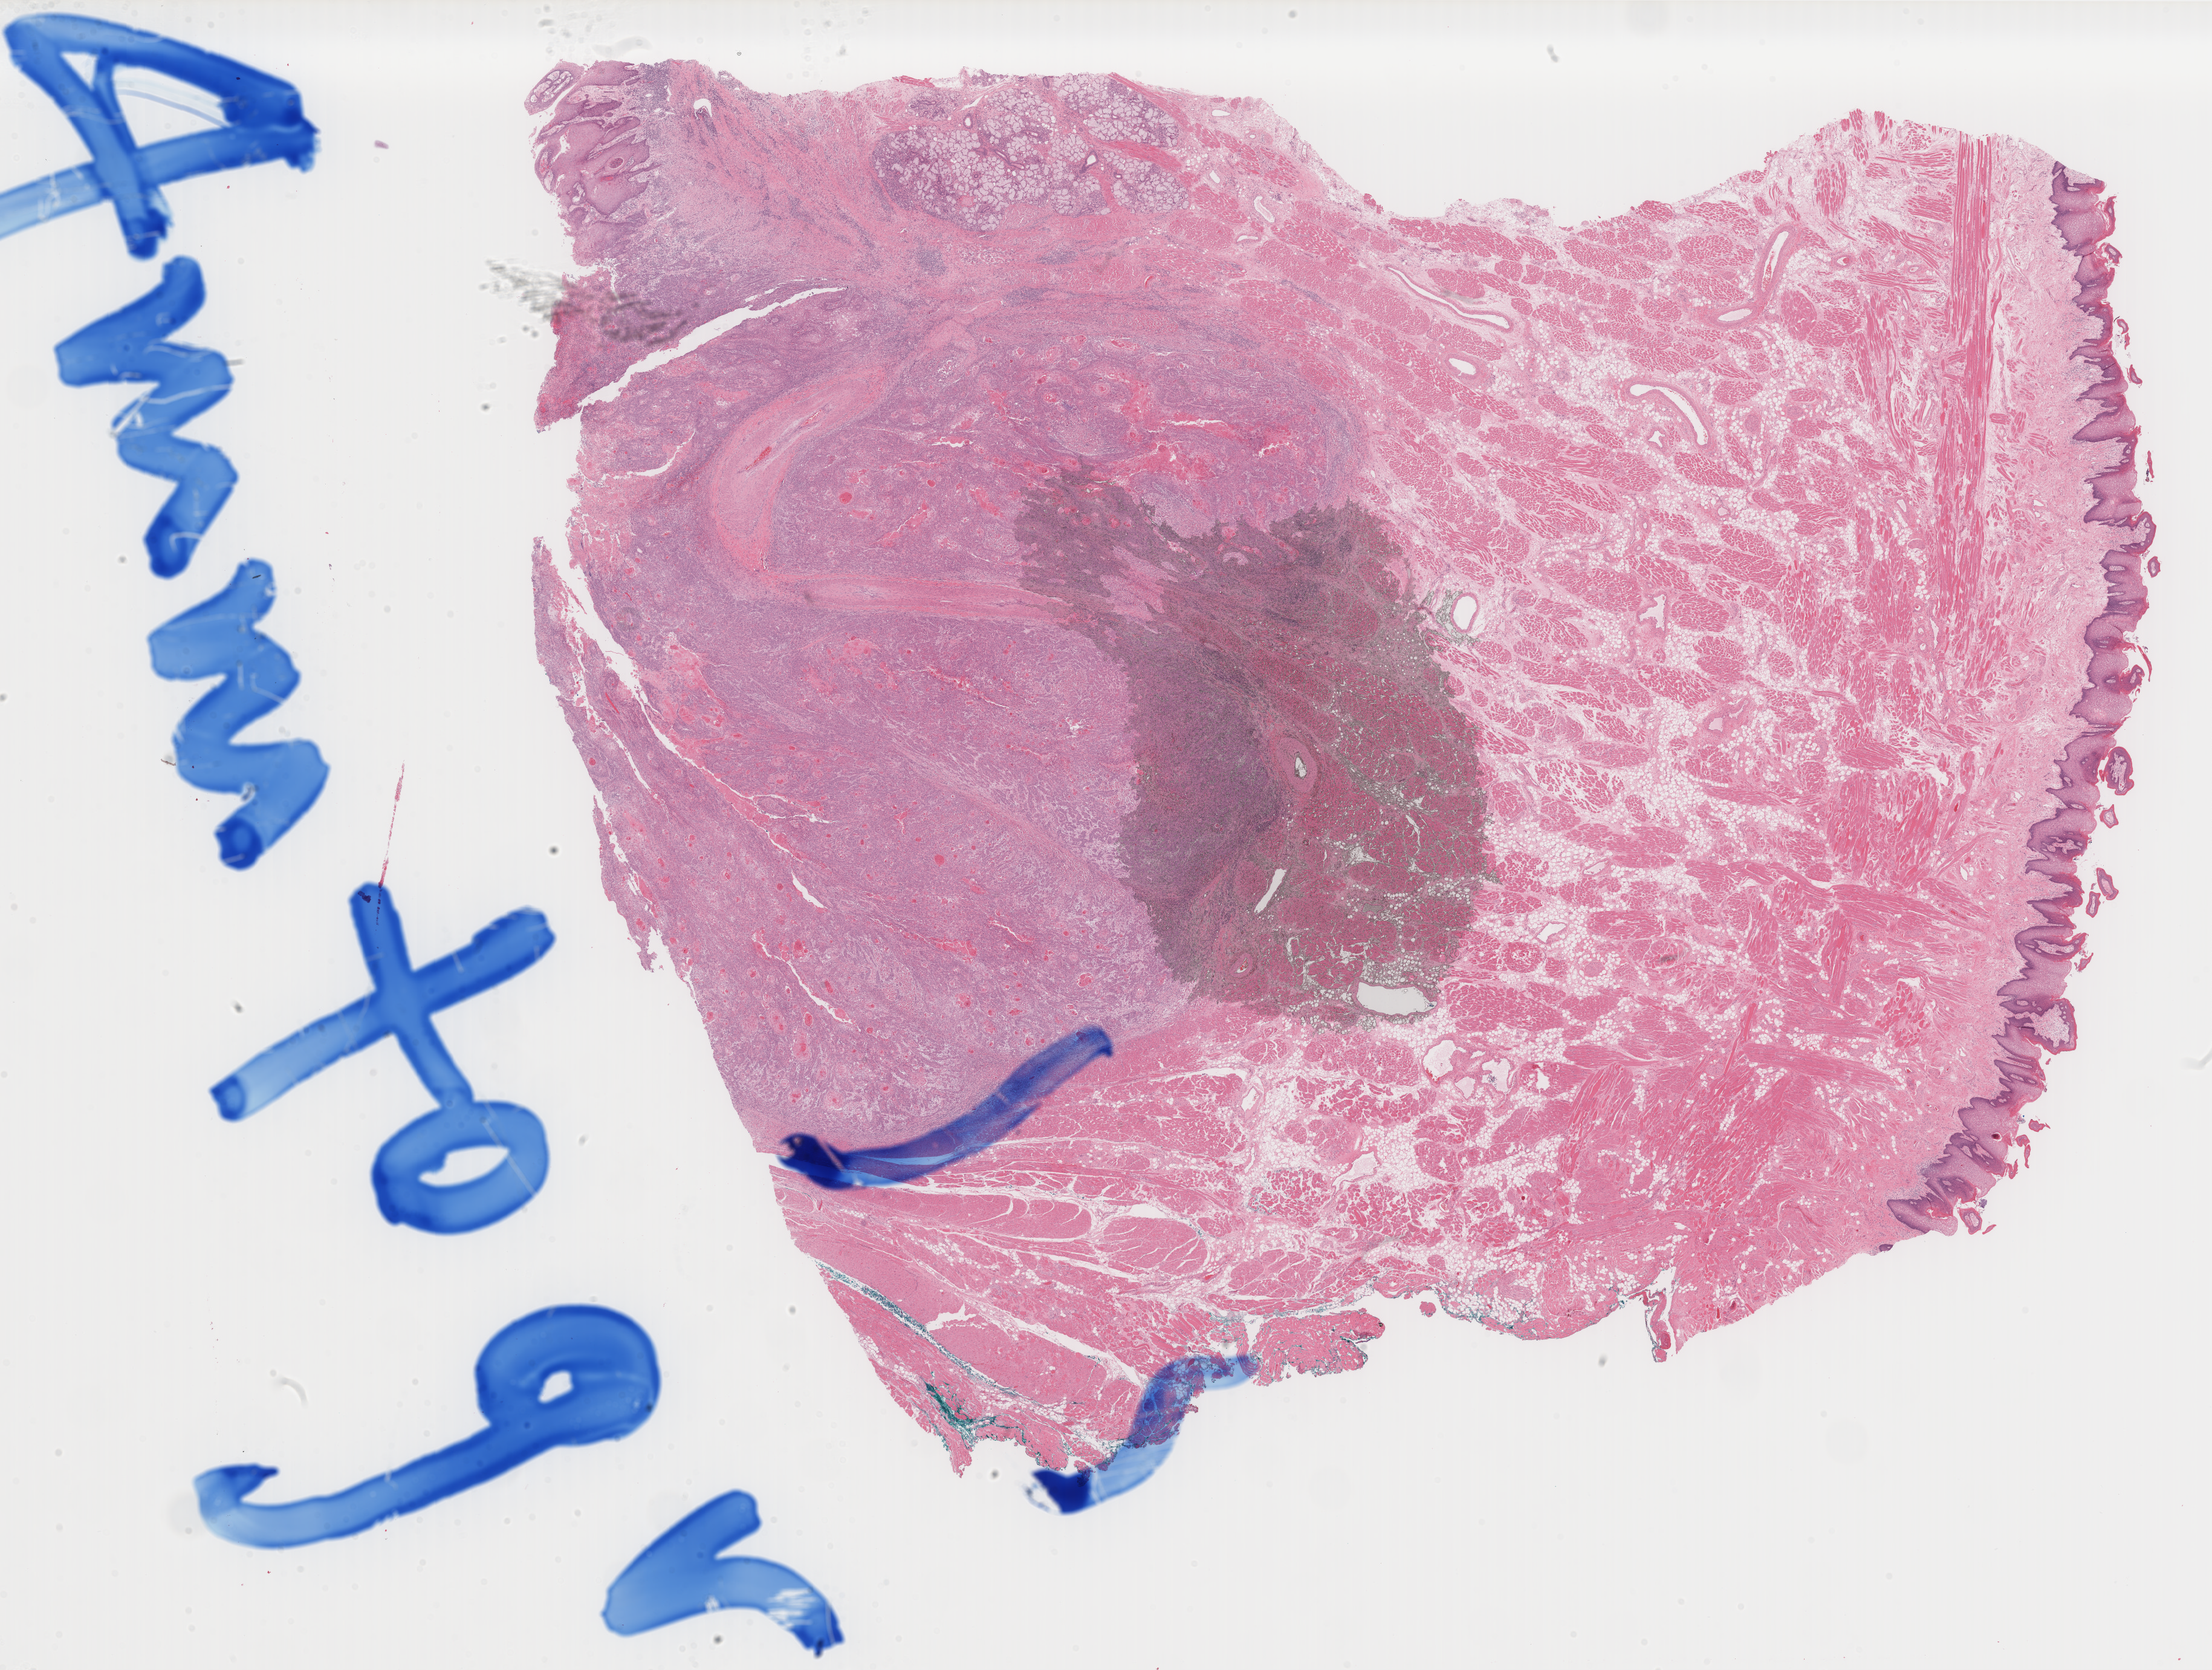
Whole-slide histology image, Hematoxylin and eosin (H&E) stained — low-resolution overview of the scanned area, about 28.9 x 21.8 mm (slide scanned at 40x), formalin-fixed paraffin-embedded (FFPE) diagnostic section, primary tumour sample from the head and neck. Male patient; age at initial diagnosis 44 years. Histologic grade: G2 (moderately differentiated).
- AJCC pathologic stage: IVA (7th edition)
- pathologic diagnosis: Squamous cell carcinoma, keratinizing, NOS